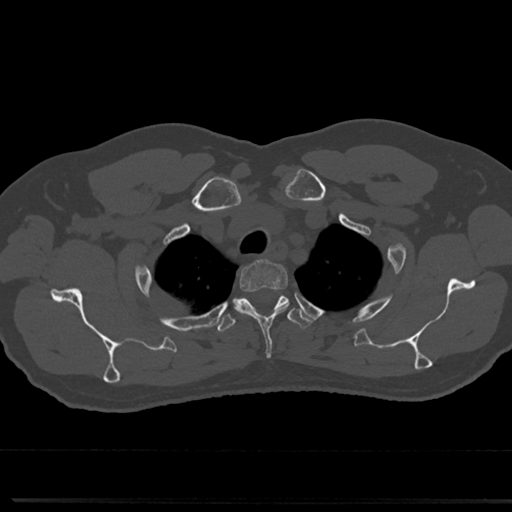
CT including the spine, one axial slice; slice 615 of 817 in the series (ordered by position); reconstruction kernel Br40s/3; 120 kVp; bone window (W 1800 / L 400 HU); 512 × 512 image matrix. Patient: male, 61 years. Case-level facts recorded for this patient, not image findings: primary cancer: prostate.
Outlined on this slice (semi-automatic segmentation, software-assisted and operator-edited):
- T2 vertebra: bounding box <239,261,289,290> (left, top, right, bottom; pixels)
- T3 vertebra: <214,292,313,334>